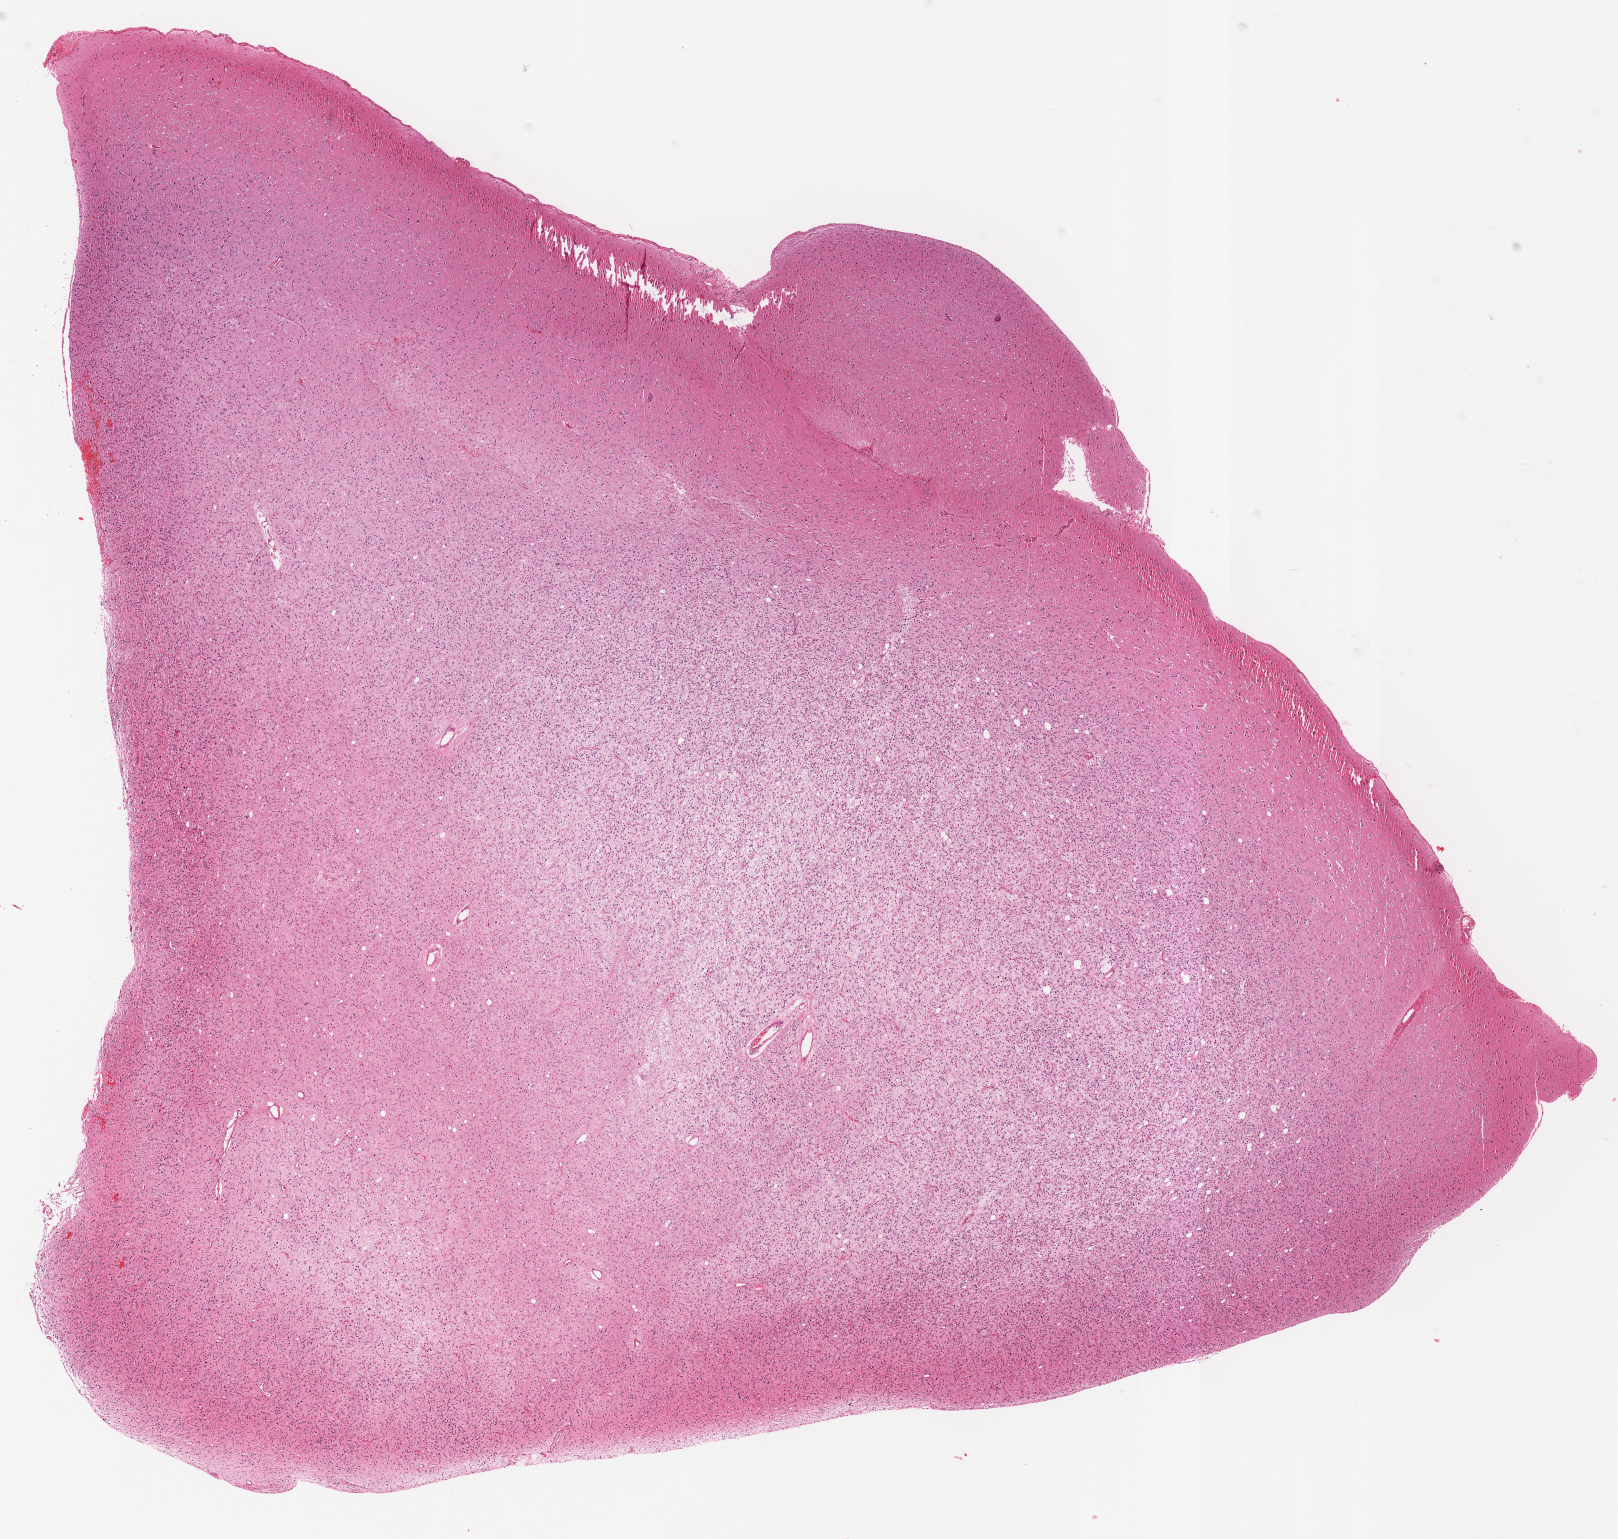
Digitized Hematoxylin and eosin (H&E) stained tissue section (whole slide) — a low-resolution overview of the entire scanned area, about 13.1 x 12.4 mm. Formalin-fixed paraffin-embedded (FFPE) diagnostic section. Primary tumour sample from the brain. Male patient; age at initial diagnosis 41 years. Histologic grade: G2 (moderately differentiated).
Histologic diagnosis: Mixed glioma.